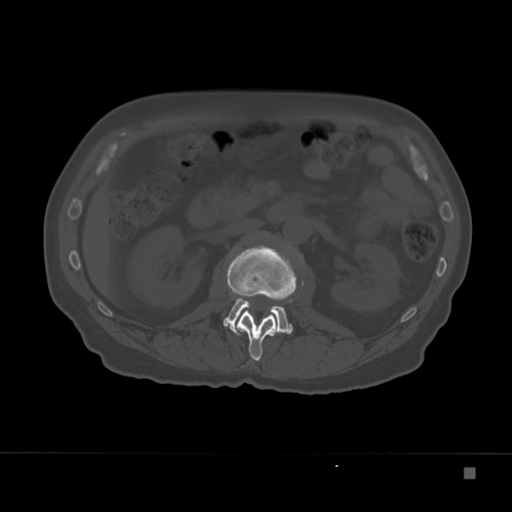
CT including the spine, one axial slice. Slice 101 of 332 in the series (ordered by position). 120 kVp. Bone window (W 1800 / L 400 HU). 1.5 mm slice thickness. 512 × 512 image matrix, field of view 389 × 389 mm. Patient: male, 72 years. From the clinical record (not read from this slice): primary cancer: skeletal.
Annotated regions visible in this slice (semi-automatic segmentation, software-assisted and operator-edited):
- L1 vertebra: bounding box <227,245,297,361> (left, top, right, bottom; pixels)
- L2 vertebra: <223,298,293,334>